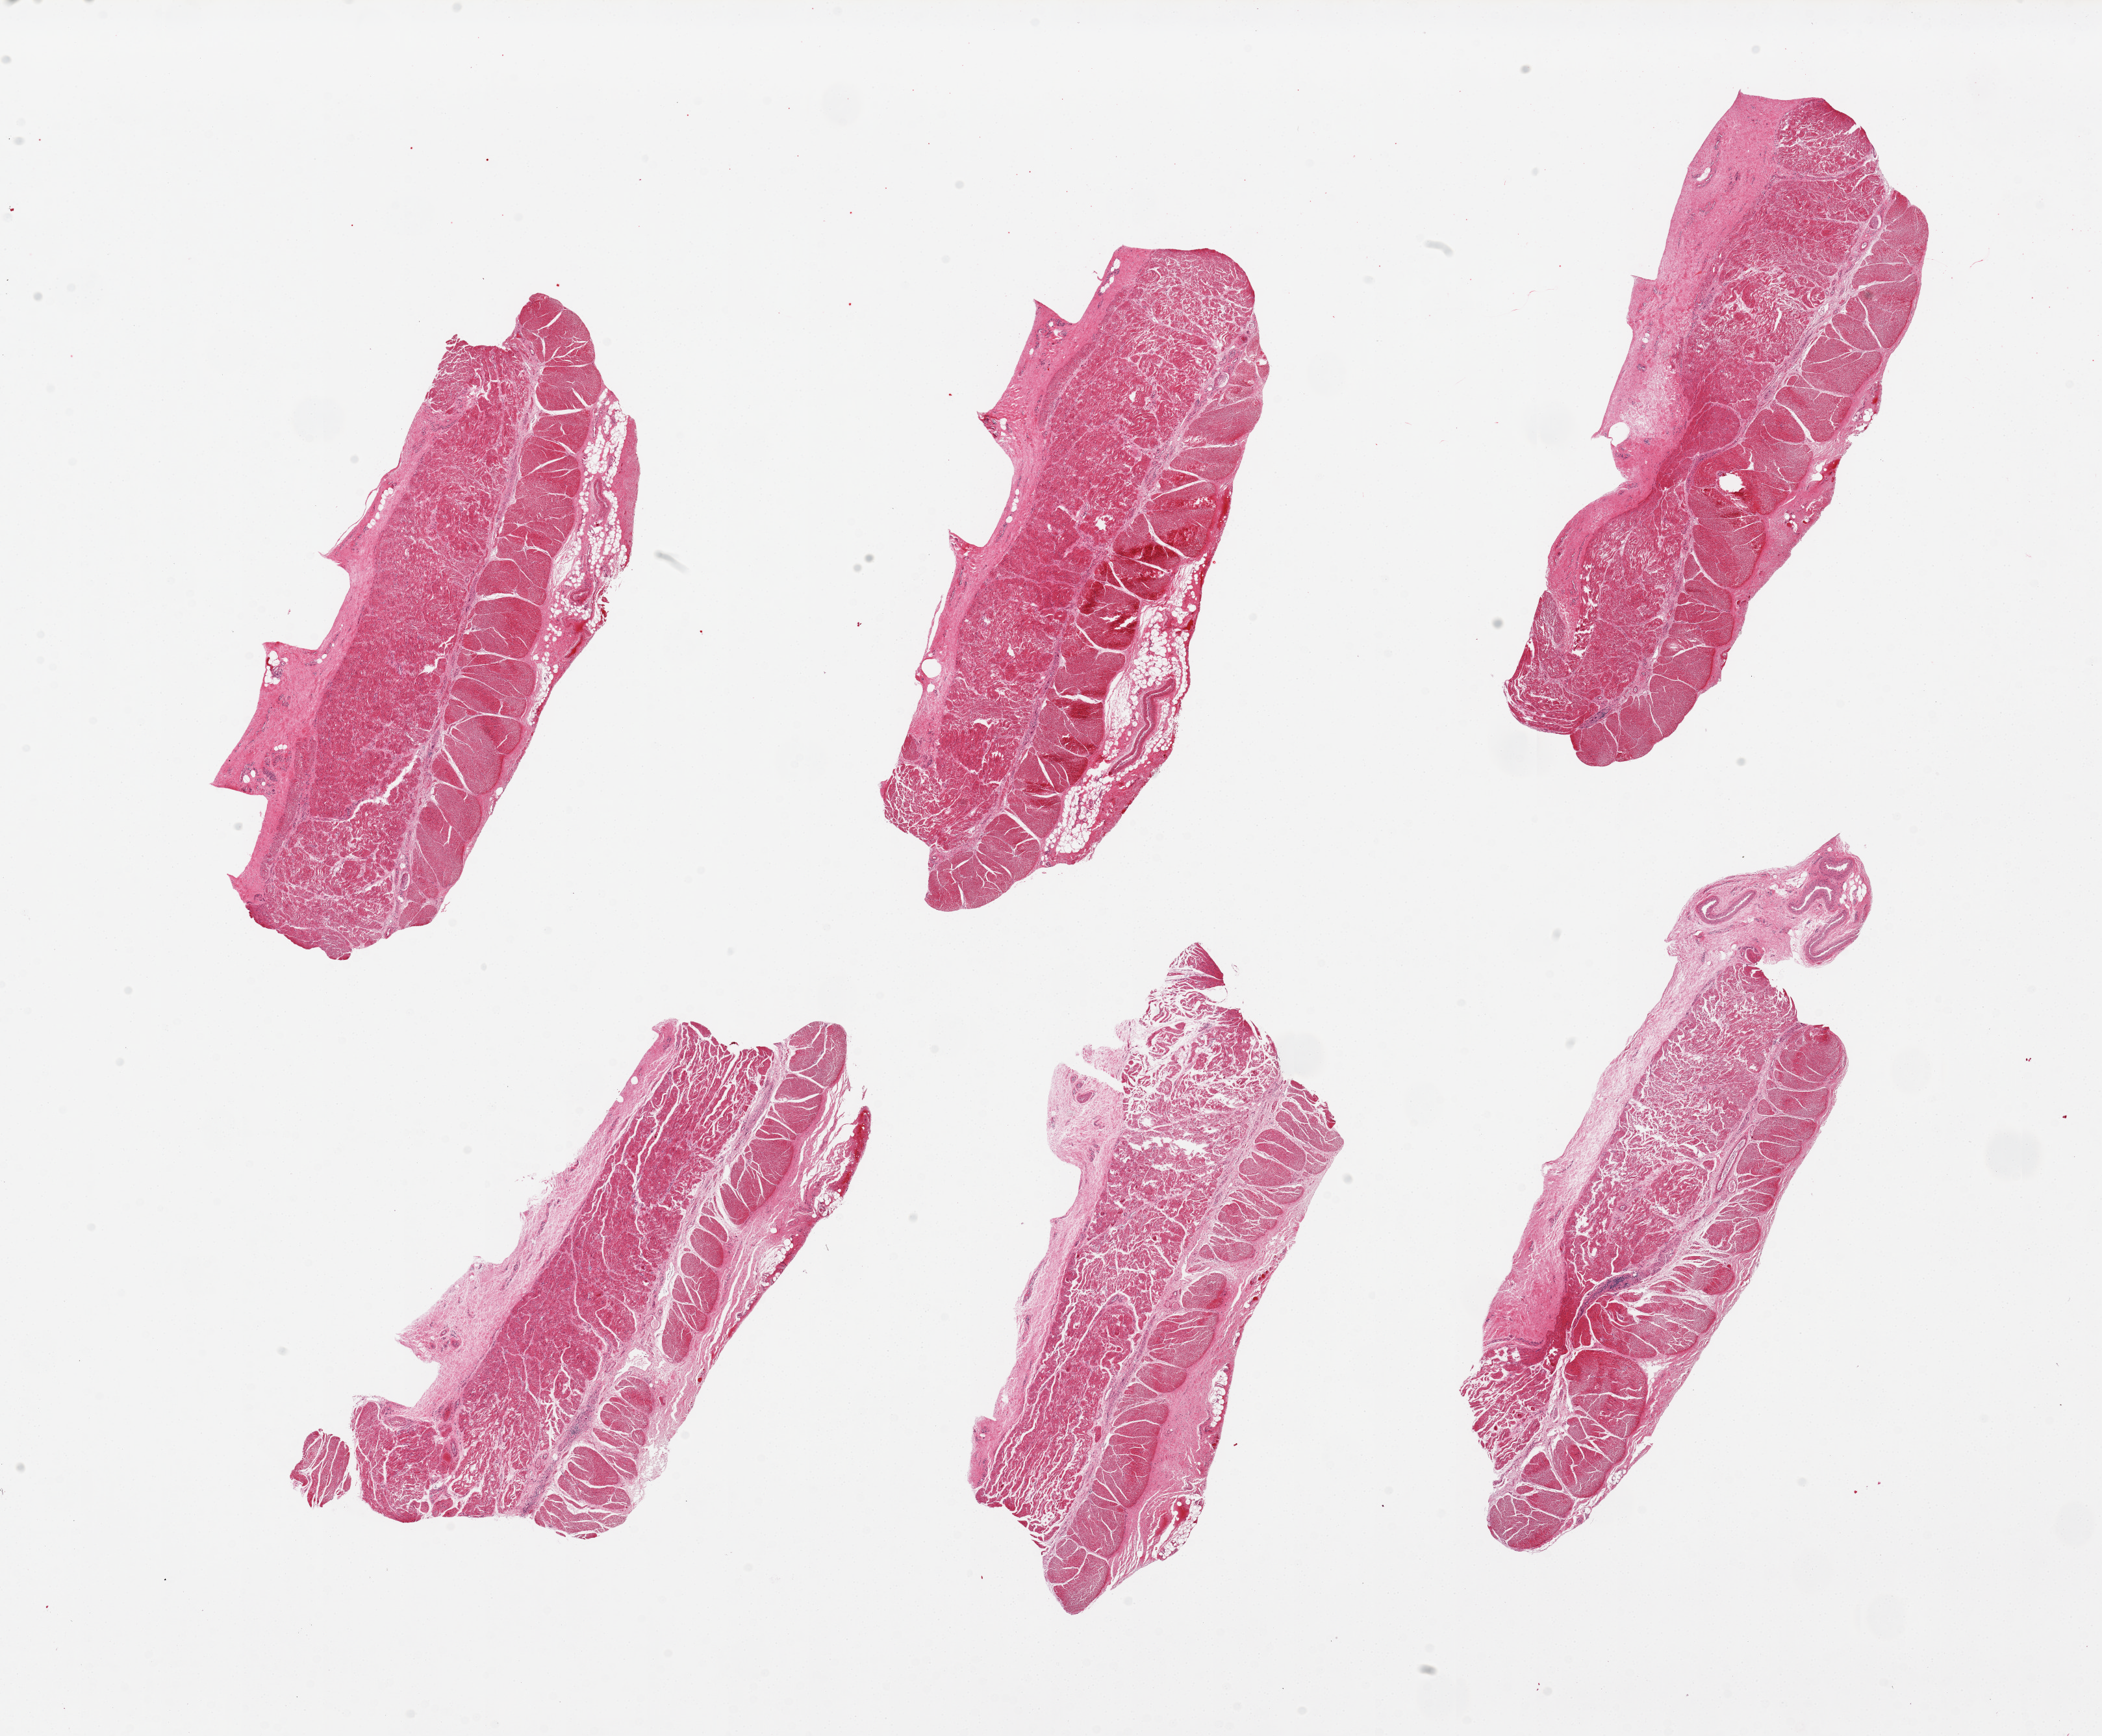
Digitized H&E-stained section, brightfield, shown as a low-resolution overview of the whole scanned area (about 25.6 x 21.1 mm, from a 20x scan), PAXgene-fixed, paraffin-embedded tissue, sampled site (target tissue): esophageal muscle, tissue donor sample. Donor: male.
Reviewer comment on this tissue sample: 6 pieces, generally all muscularis. Up to ~0.7mm adherent fatty layer on several sections.